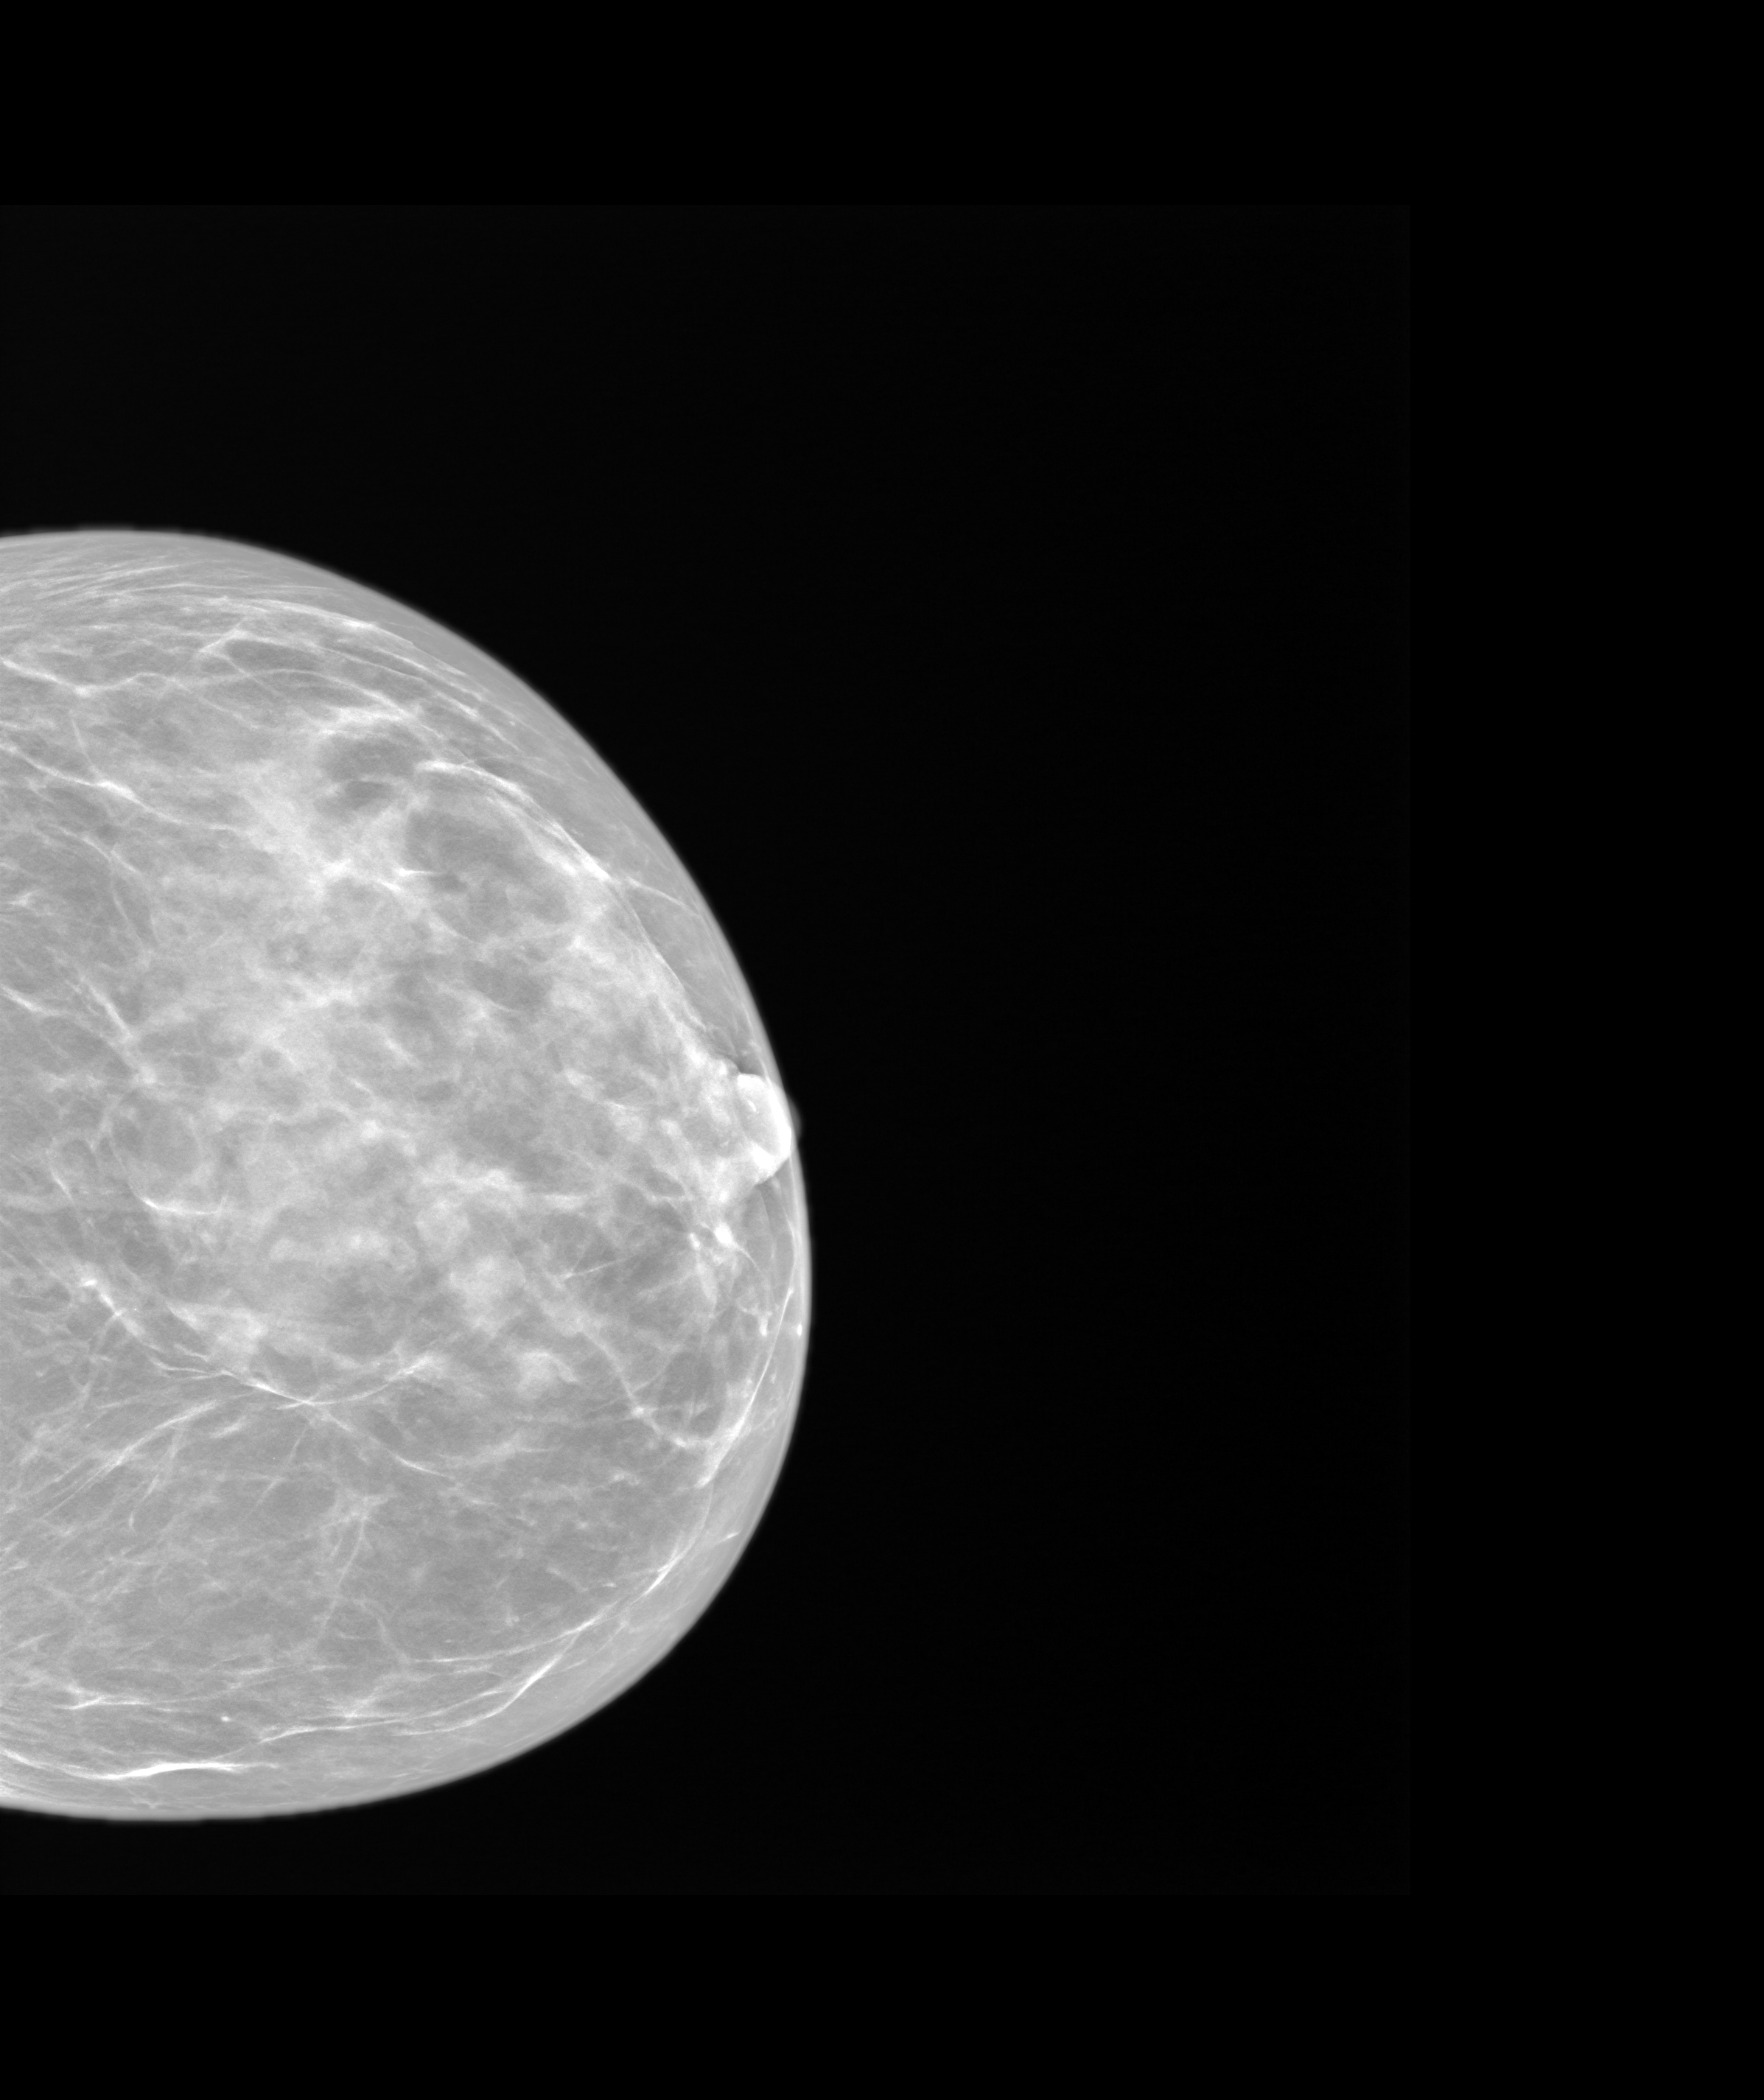
Screening examination.
Image type: synthesized 2-D view from tomosynthesis. Breast: left. Projection: cranio-caudal projection.